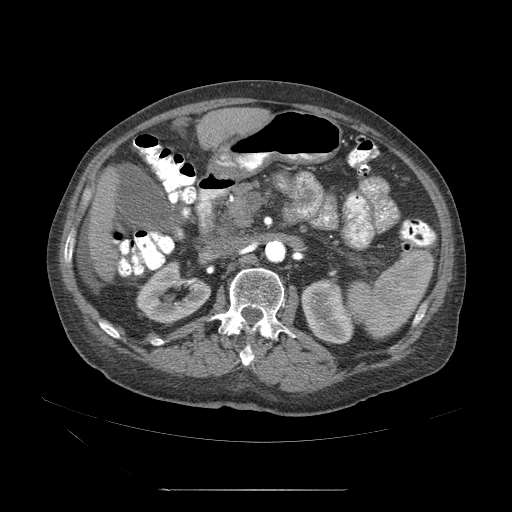
Contrast-enhanced abdominal CT (liver protocol), one axial slice. Slice 15 of 71 in the series (ordered by position). Reconstruction kernel STANDARD. Soft-tissue window (W 400 / L 40 HU). 2.5 mm slice thickness. 512 × 512 image matrix. Case-level facts recorded for this patient, not image findings: diagnosis: hepatocellular carcinoma (patient treated with transarterial chemoembolisation; whether this scan precedes or follows treatment is not stated here); TNM stage (as recorded): Stage-II; Child-Pugh class: A; tumour nodularity: multinodular; tumour size: 1 cm.
Outlined on this slice (semi-automatically segmented with operator editing):
- abdominal aorta: bounding box <265,242,286,264> (left, top, right, bottom; pixels)